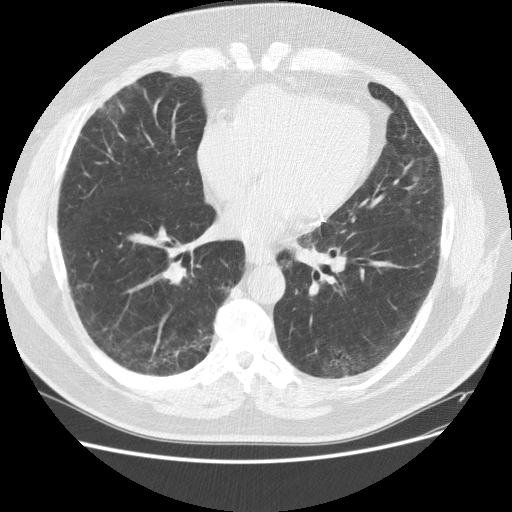
Chest CT (low-dose screening protocol), one axial image. Baseline annual screen. Lung window (W 1500 / L -600 HU). 2.5 mm slice thickness. Slice 80 of 151 in the series. Male, age 59 years at enrolment.
Expert-annotated lung lesion, box from (x=85, y=87) to (x=131, y=139) px. The screening reader recorded 2 non-calcified nodules or masses ≥4 mm on this exam; which of them this box marks is not recorded.